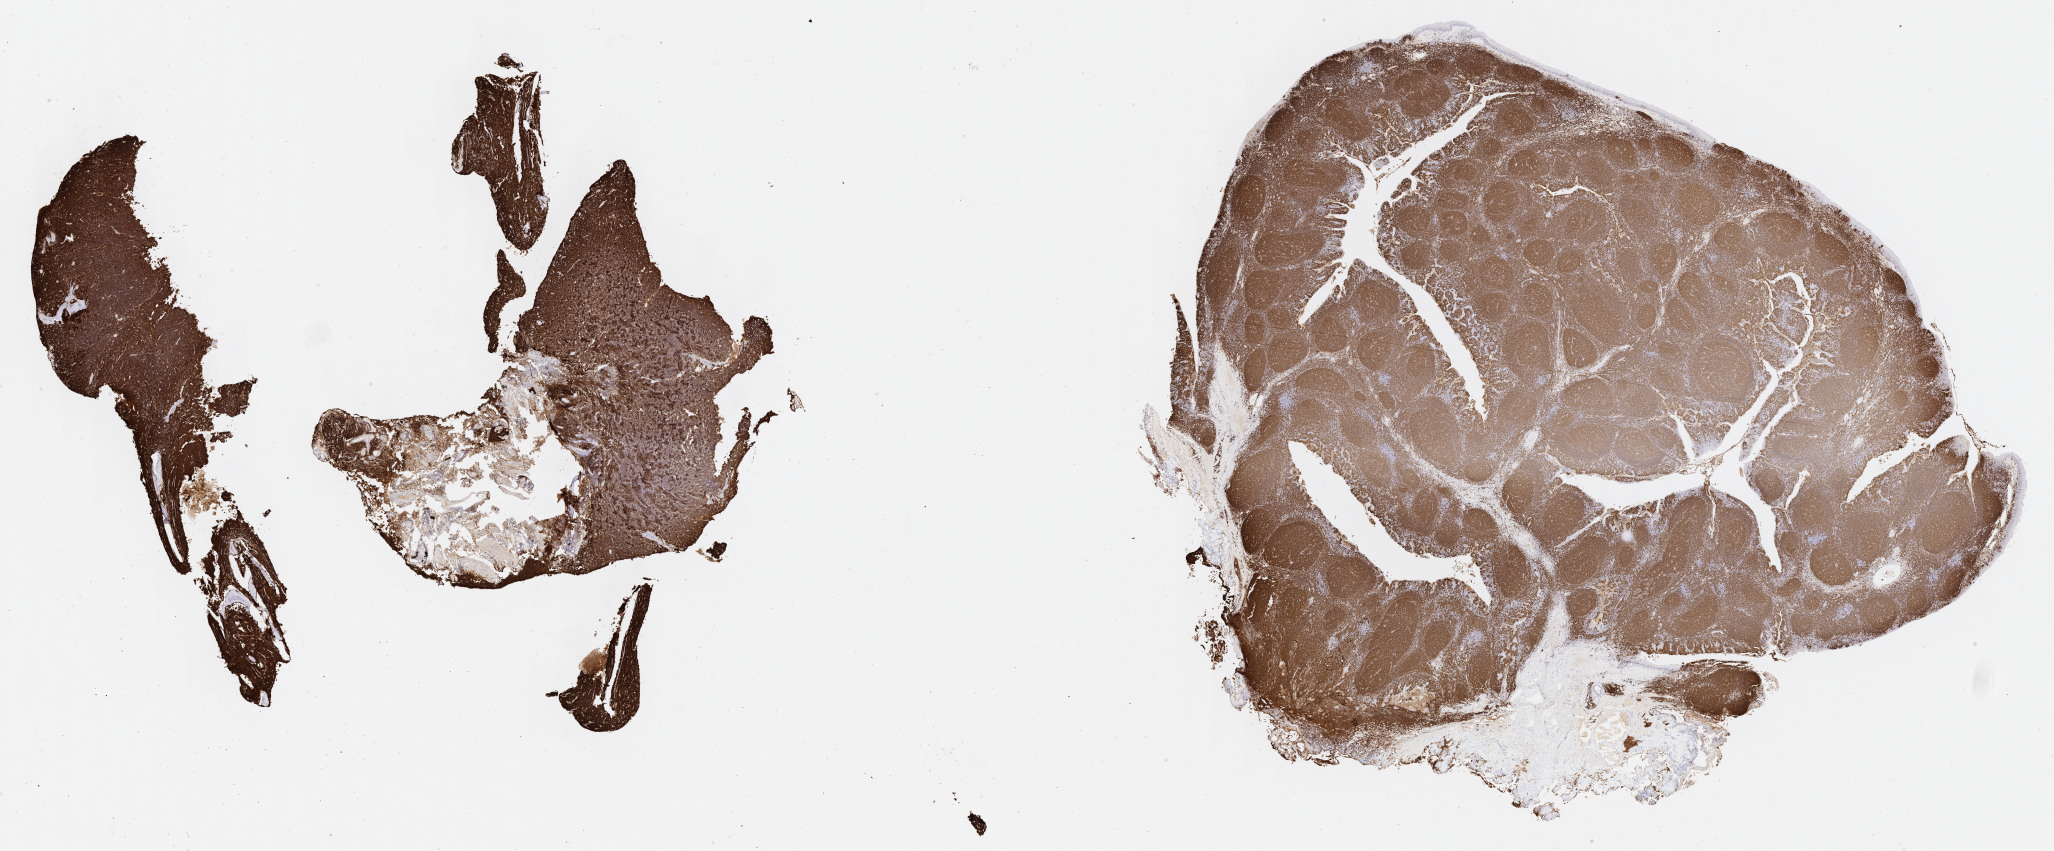
IHC for CD20, whole-slide image — a low-resolution overview of the entire scanned area, about 33.2 x 13.8 mm. Specimen: tumor tissue. Anatomic site: cranium. Patient: male, age at initial diagnosis 8 years.
* diagnosis: Burkitt lymphoma, NOS